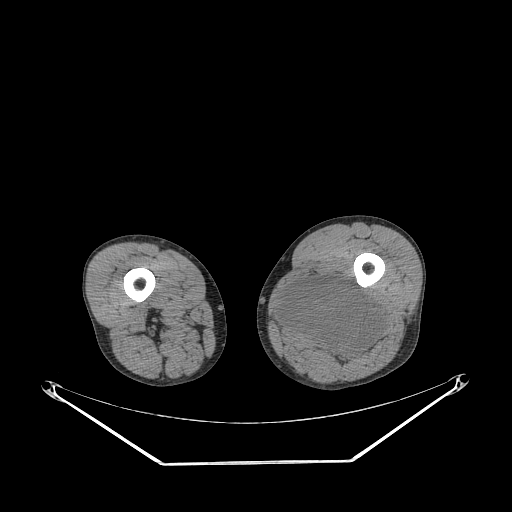
CT of an extremity soft-tissue mass (from a PET/CT study), one axial slice. Slice 226 of 267 in the series (ordered by position). Reconstruction kernel STANDARD. Soft-tissue window (W 400 / L 40 HU). 512 × 512 image matrix. Male patient. Case-level facts recorded for this patient, not image findings: histological type: undifferentiated pleomorphic liposarcoma; grade: high; site of the primary tumour: left thigh.
Outlined on this slice (expert contour drawn on MRI and transferred to this co-registered scan by the dataset authors):
- gross tumour volume including surrounding oedema: bounding box <278,278,384,362> (left, top, right, bottom; pixels)
- gross tumour volume (mass): <279,278,384,362>